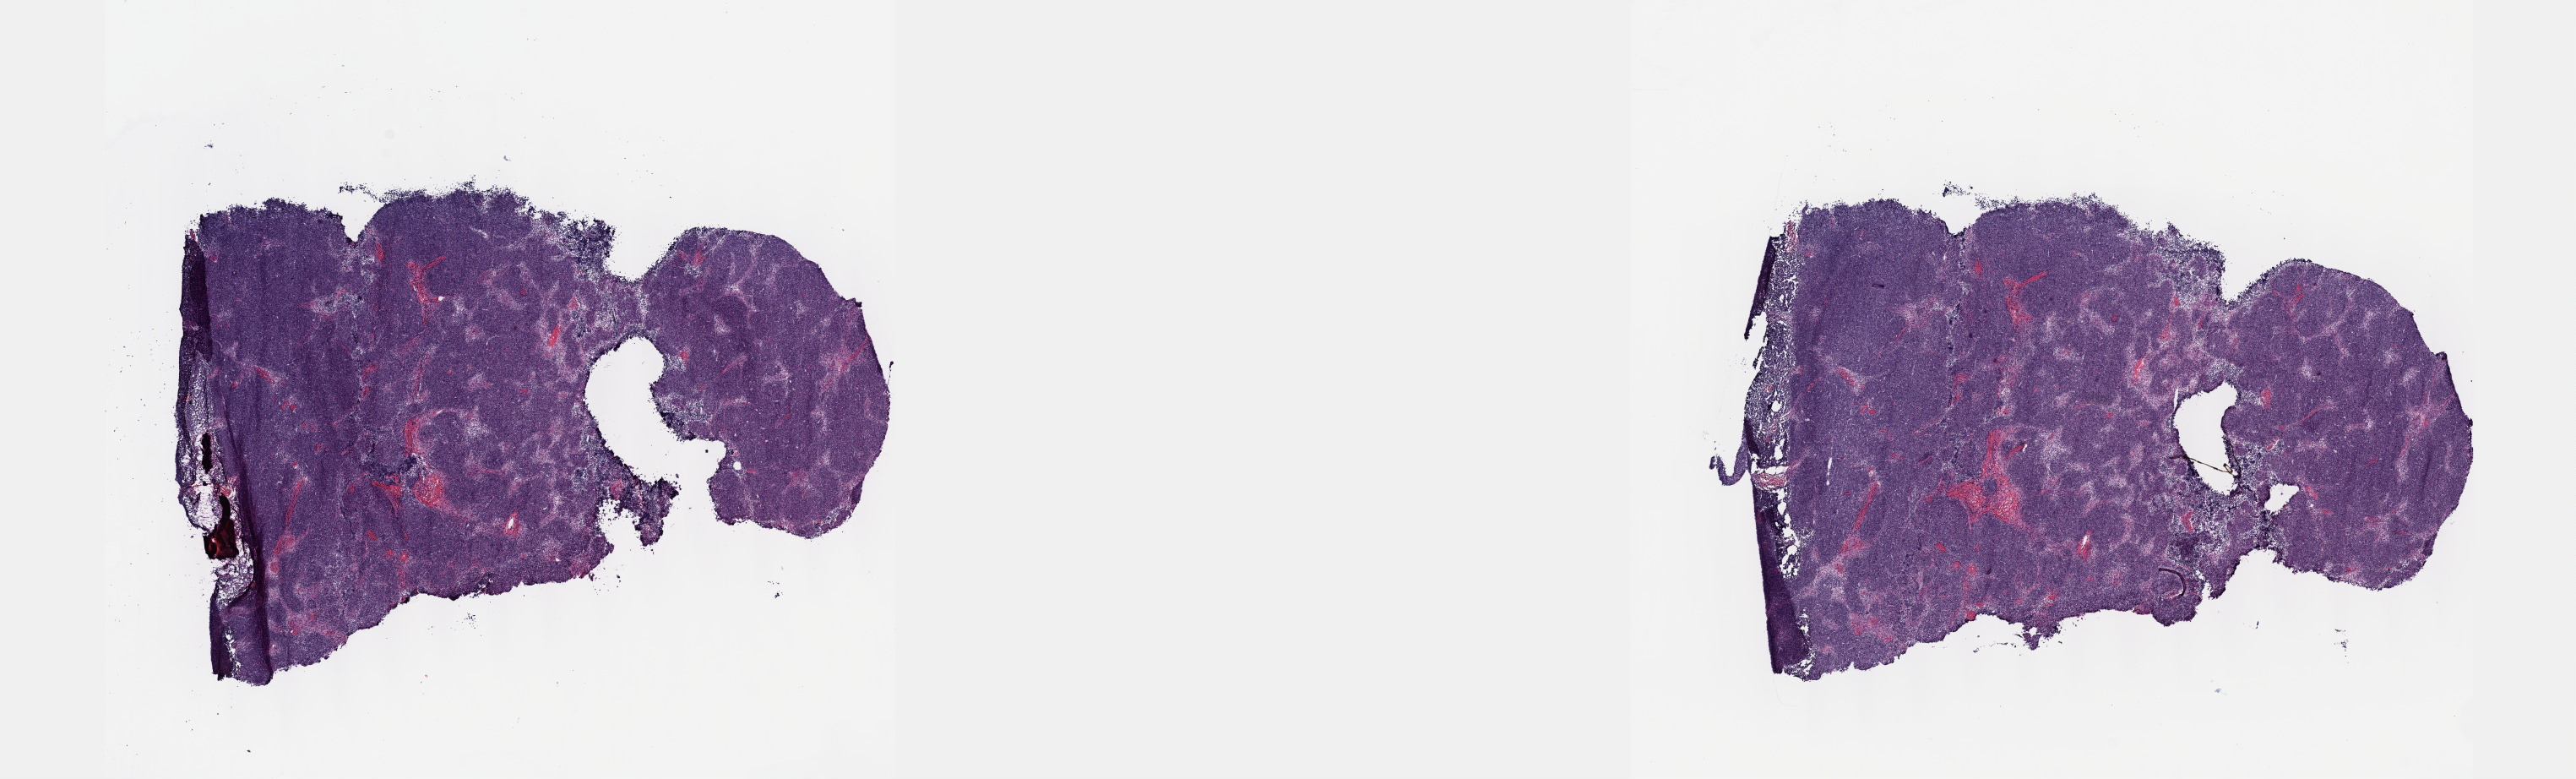
Hematoxylin and eosin (H&E) stained whole-slide image — shown as a low-resolution overview of the whole scanned area (about 24.6 x 7.5 mm). Frozen section from the top of the tissue portion. Primary tumour sample from the thymus. Patient: female, age at initial diagnosis 57 years. Slide review estimates, as recorded: tumour cells 98%, tumour nuclei 98%, normal cells 0%, stromal cells 2%, necrosis 0%. Inflammatory infiltration, as recorded: lymphocyte infiltration 0%, monocyte infiltration 0%, neutrophil infiltration 0%.
Diagnosis: Thymoma, type AB, malignant.